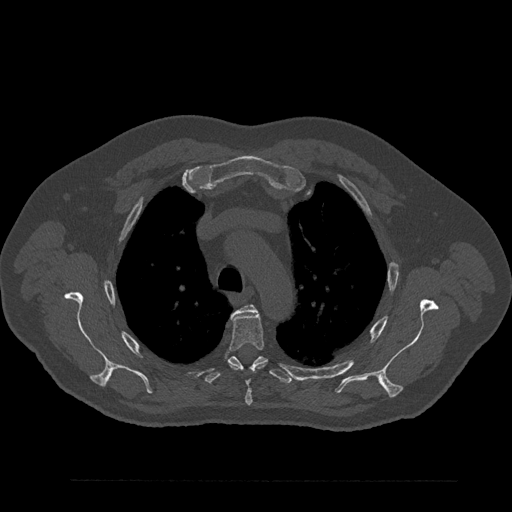
CT including the spine, one axial slice; reconstruction kernel Br40s/3; 120 kVp; bone window (W 1800 / L 400 HU); 0.5 mm slice thickness; 512 × 512 image matrix, field of view 430 × 430 mm. Male patient, age 61 years. From the clinical record (not read from this slice): primary cancer: prostate.
Outlined on this slice (semi-automatic segmentation, software-assisted and operator-edited):
- T3 vertebra: bounding box (x1, y1, x2, y2) in pixels: (233, 304, 257, 314)
- T4 vertebra: (228, 313, 265, 406)
- T5 vertebra: (204, 356, 292, 384)